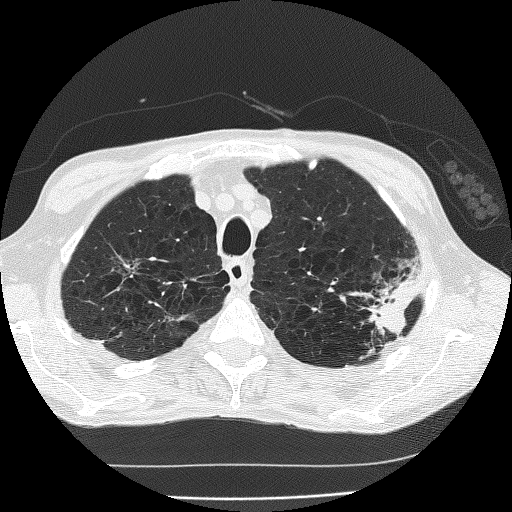
Chest CT (low-dose screening protocol), one axial image. Second screening round (one year after baseline). Lung window (W 1500 / L -600 HU). Lung (sharp) reconstruction kernel (FC51). Slice 35 of 185 in the series. 512 × 512 image matrix. Male, age 60 years at enrolment. Current smoker at enrolment.
Lesion marked by an expert reader, box from (x=346, y=266) to (x=424, y=341) px. The screening reader recorded 2 non-calcified nodules or masses ≥4 mm on this exam (left upper lobe, left upper lobe); which of them this box marks is not recorded. Official screen result: positive, other. Lung cancer was diagnosed 178 days after this screen: bronchiolo-alveolar carcinoma, mucinous, left upper lobe, stage IV (AJCC 6th edition).